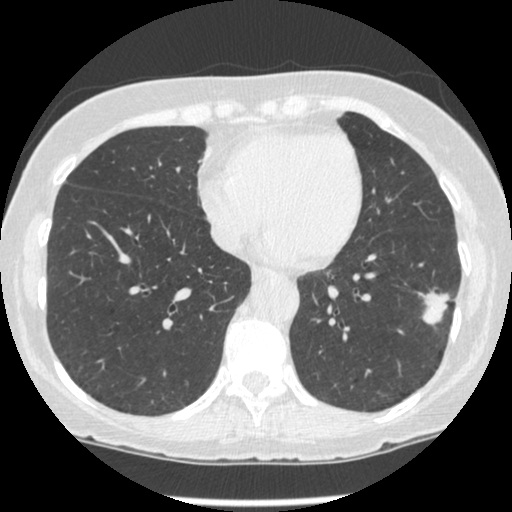
Low-dose screening chest CT, one axial slice; slice 89 of 247 in the series (ordered by position); reconstruction kernel STANDARD; lung window (W 1500 / L -600 HU); 1.25 mm slice thickness; 512 × 512 image matrix, field of view 303 × 303 mm.
Annotated regions visible in this slice (manually delineated by an expert):
- lesion 1 (tumor, lower lobe of left lung): bounding box <420,291,449,325> (left, top, right, bottom; pixels)